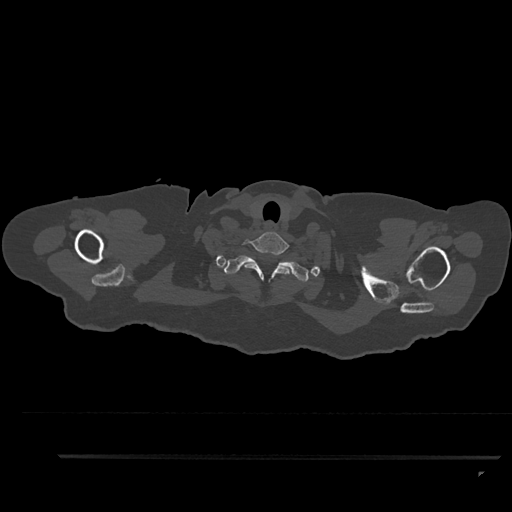
CT including the spine, one axial slice. Slice 780 of 797 in the series (ordered by position). Reconstruction kernel Br40s/3. Bone window (W 1800 / L 400 HU). 0.5 mm slice thickness. 512 × 512 image matrix, field of view 408 × 408 mm. Female patient, age 44 years. Case-level facts recorded for this patient, not image findings: primary cancer: renal; vertebrae with lytic lesions (as recorded): L1.
Annotated regions visible in this slice (semi-automatic segmentation, software-assisted and operator-edited):
- T1 vertebra: bounding box (x1, y1, x2, y2) in pixels: (224, 255, 309, 282)